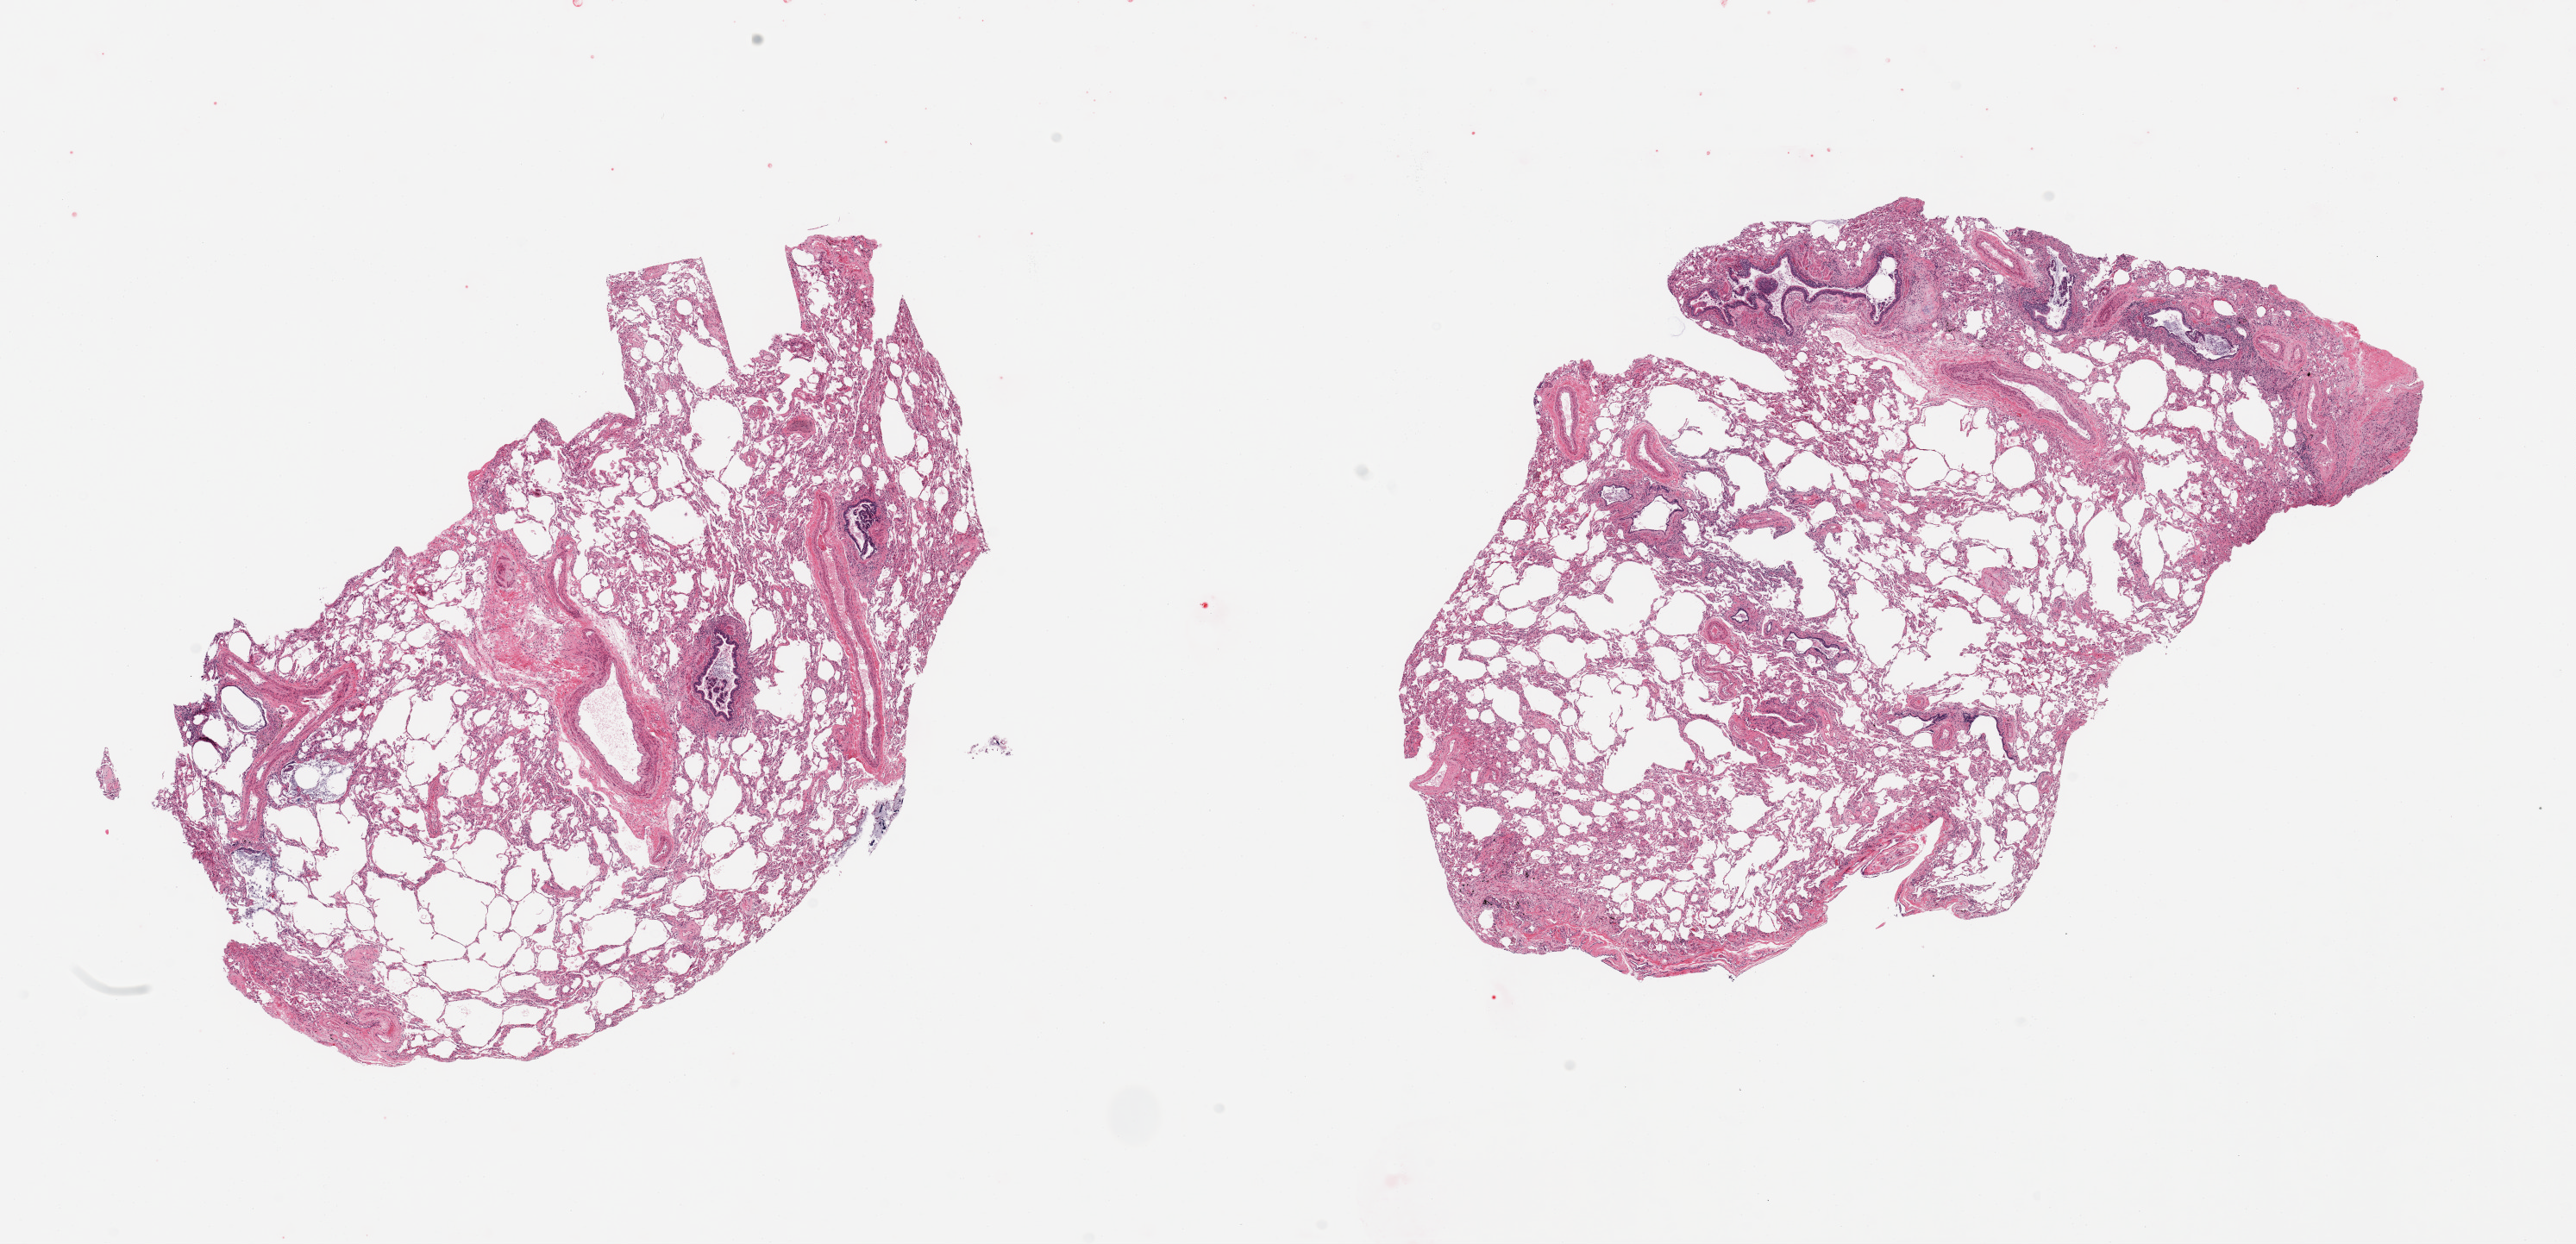
Whole-slide image, H&E stain, a low-resolution overview of the entire scanned area, about 23.6 x 11.4 mm, PAXgene-fixed paraffin-embedded (PFPE) section, sampled site (target tissue): lung, tissue donor sample.
- reviewer comment on this tissue sample: 2 pieces; emphysematous change